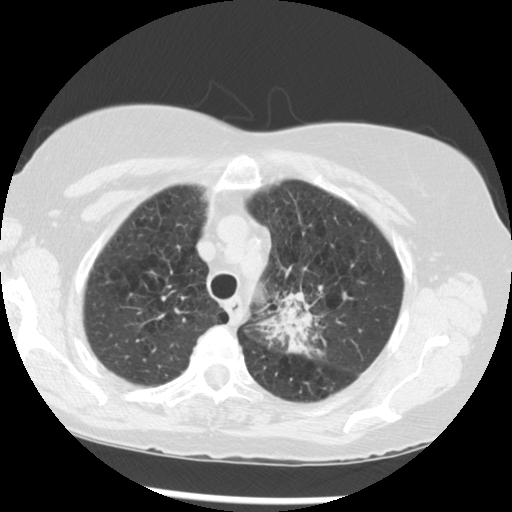
Low-dose screening chest CT, axial slice. Third annual screen. Lung window (W 1500 / L -600 HU). 120 kVp. 512 × 512 image matrix, field of view 330 × 330 mm. Female participant, aged 70 years at enrolment.
Expert-annotated lung lesion, bounding box <259,276,355,365> (left, top, right, bottom; pixels). Reader record for this screening exam (exam-level; its link to the box is not recorded): non-calcified nodule or mass ≥4 mm, left upper lobe, 32 × 26 mm, spiculated (stellate) margins, soft tissue attenuation, pre-existing on the prior screen: yes; interval growth: yes. Later outcome: lung cancer diagnosed 24 days after this screen — neoplasm, malignant, left upper lobe, stage IIIB (AJCC 6th edition), 40 mm at pathology.